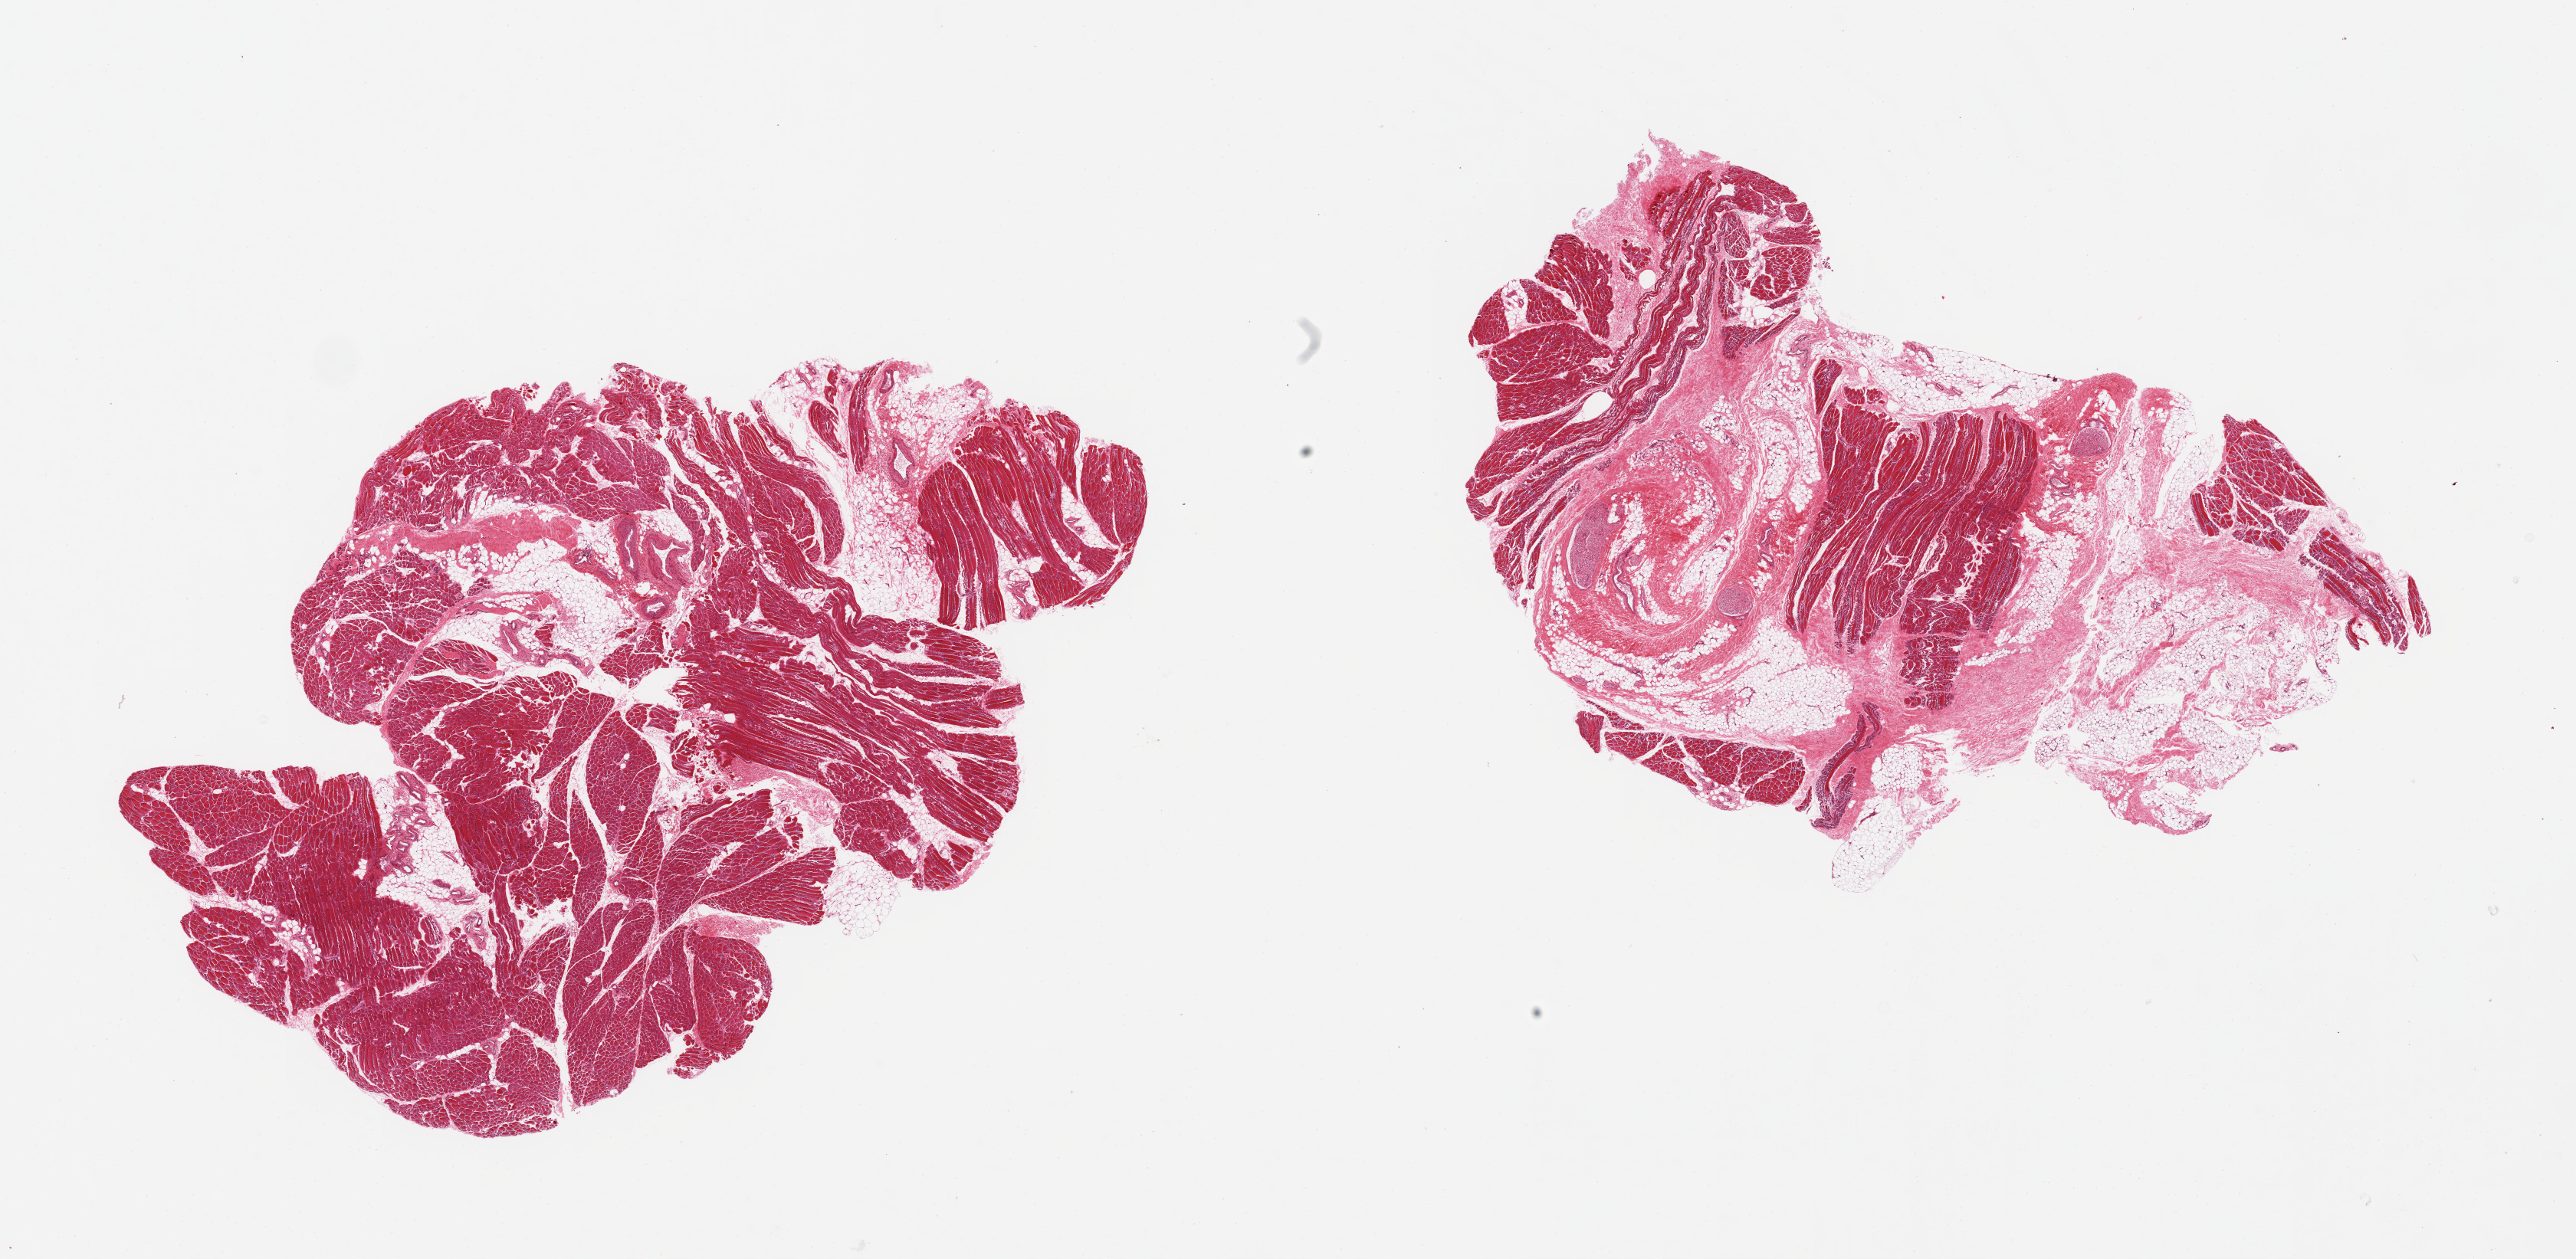
Hematoxylin and eosin (H&E) whole-slide image — shown as a low-resolution overview of the whole scanned area (about 26.6 x 13.0 mm, acquisition: 20x scan). PAXgene-fixed paraffin-embedded (PFPE) section. Section of skeletal muscle (target tissue). Tissue donor sample. Donor: female.
• review note (as recorded): 2 pieces, beware ~40% interstitial fat/fascia